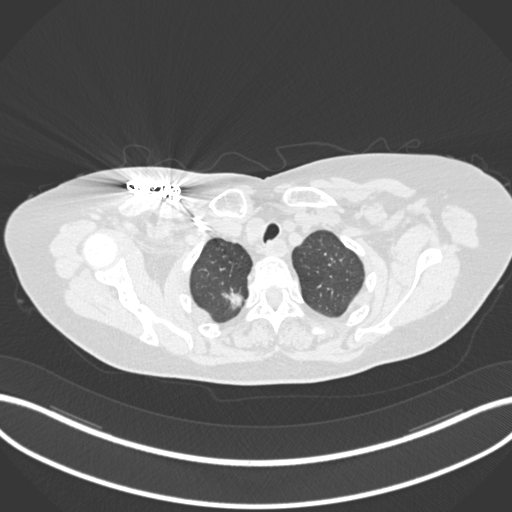
Chest CT, one axial slice. Slice 159 of 176 in the series (ordered by position). Reconstruction kernel B30f. 120 kVp. Lung window (W 1500 / L -600 HU). 1 mm slice thickness. 512 × 512 image matrix. Female patient, age 72 years. From the clinical record (not read from this slice): clinical TNM (as recorded): T1c N0 M0.
Structures marked on this image (rectangle marked by the reading radiologist):
- lung tumour (recorded histology: adenocarcinoma): bounding box [x1, y1, x2, y2] px = [219, 281, 245, 310]